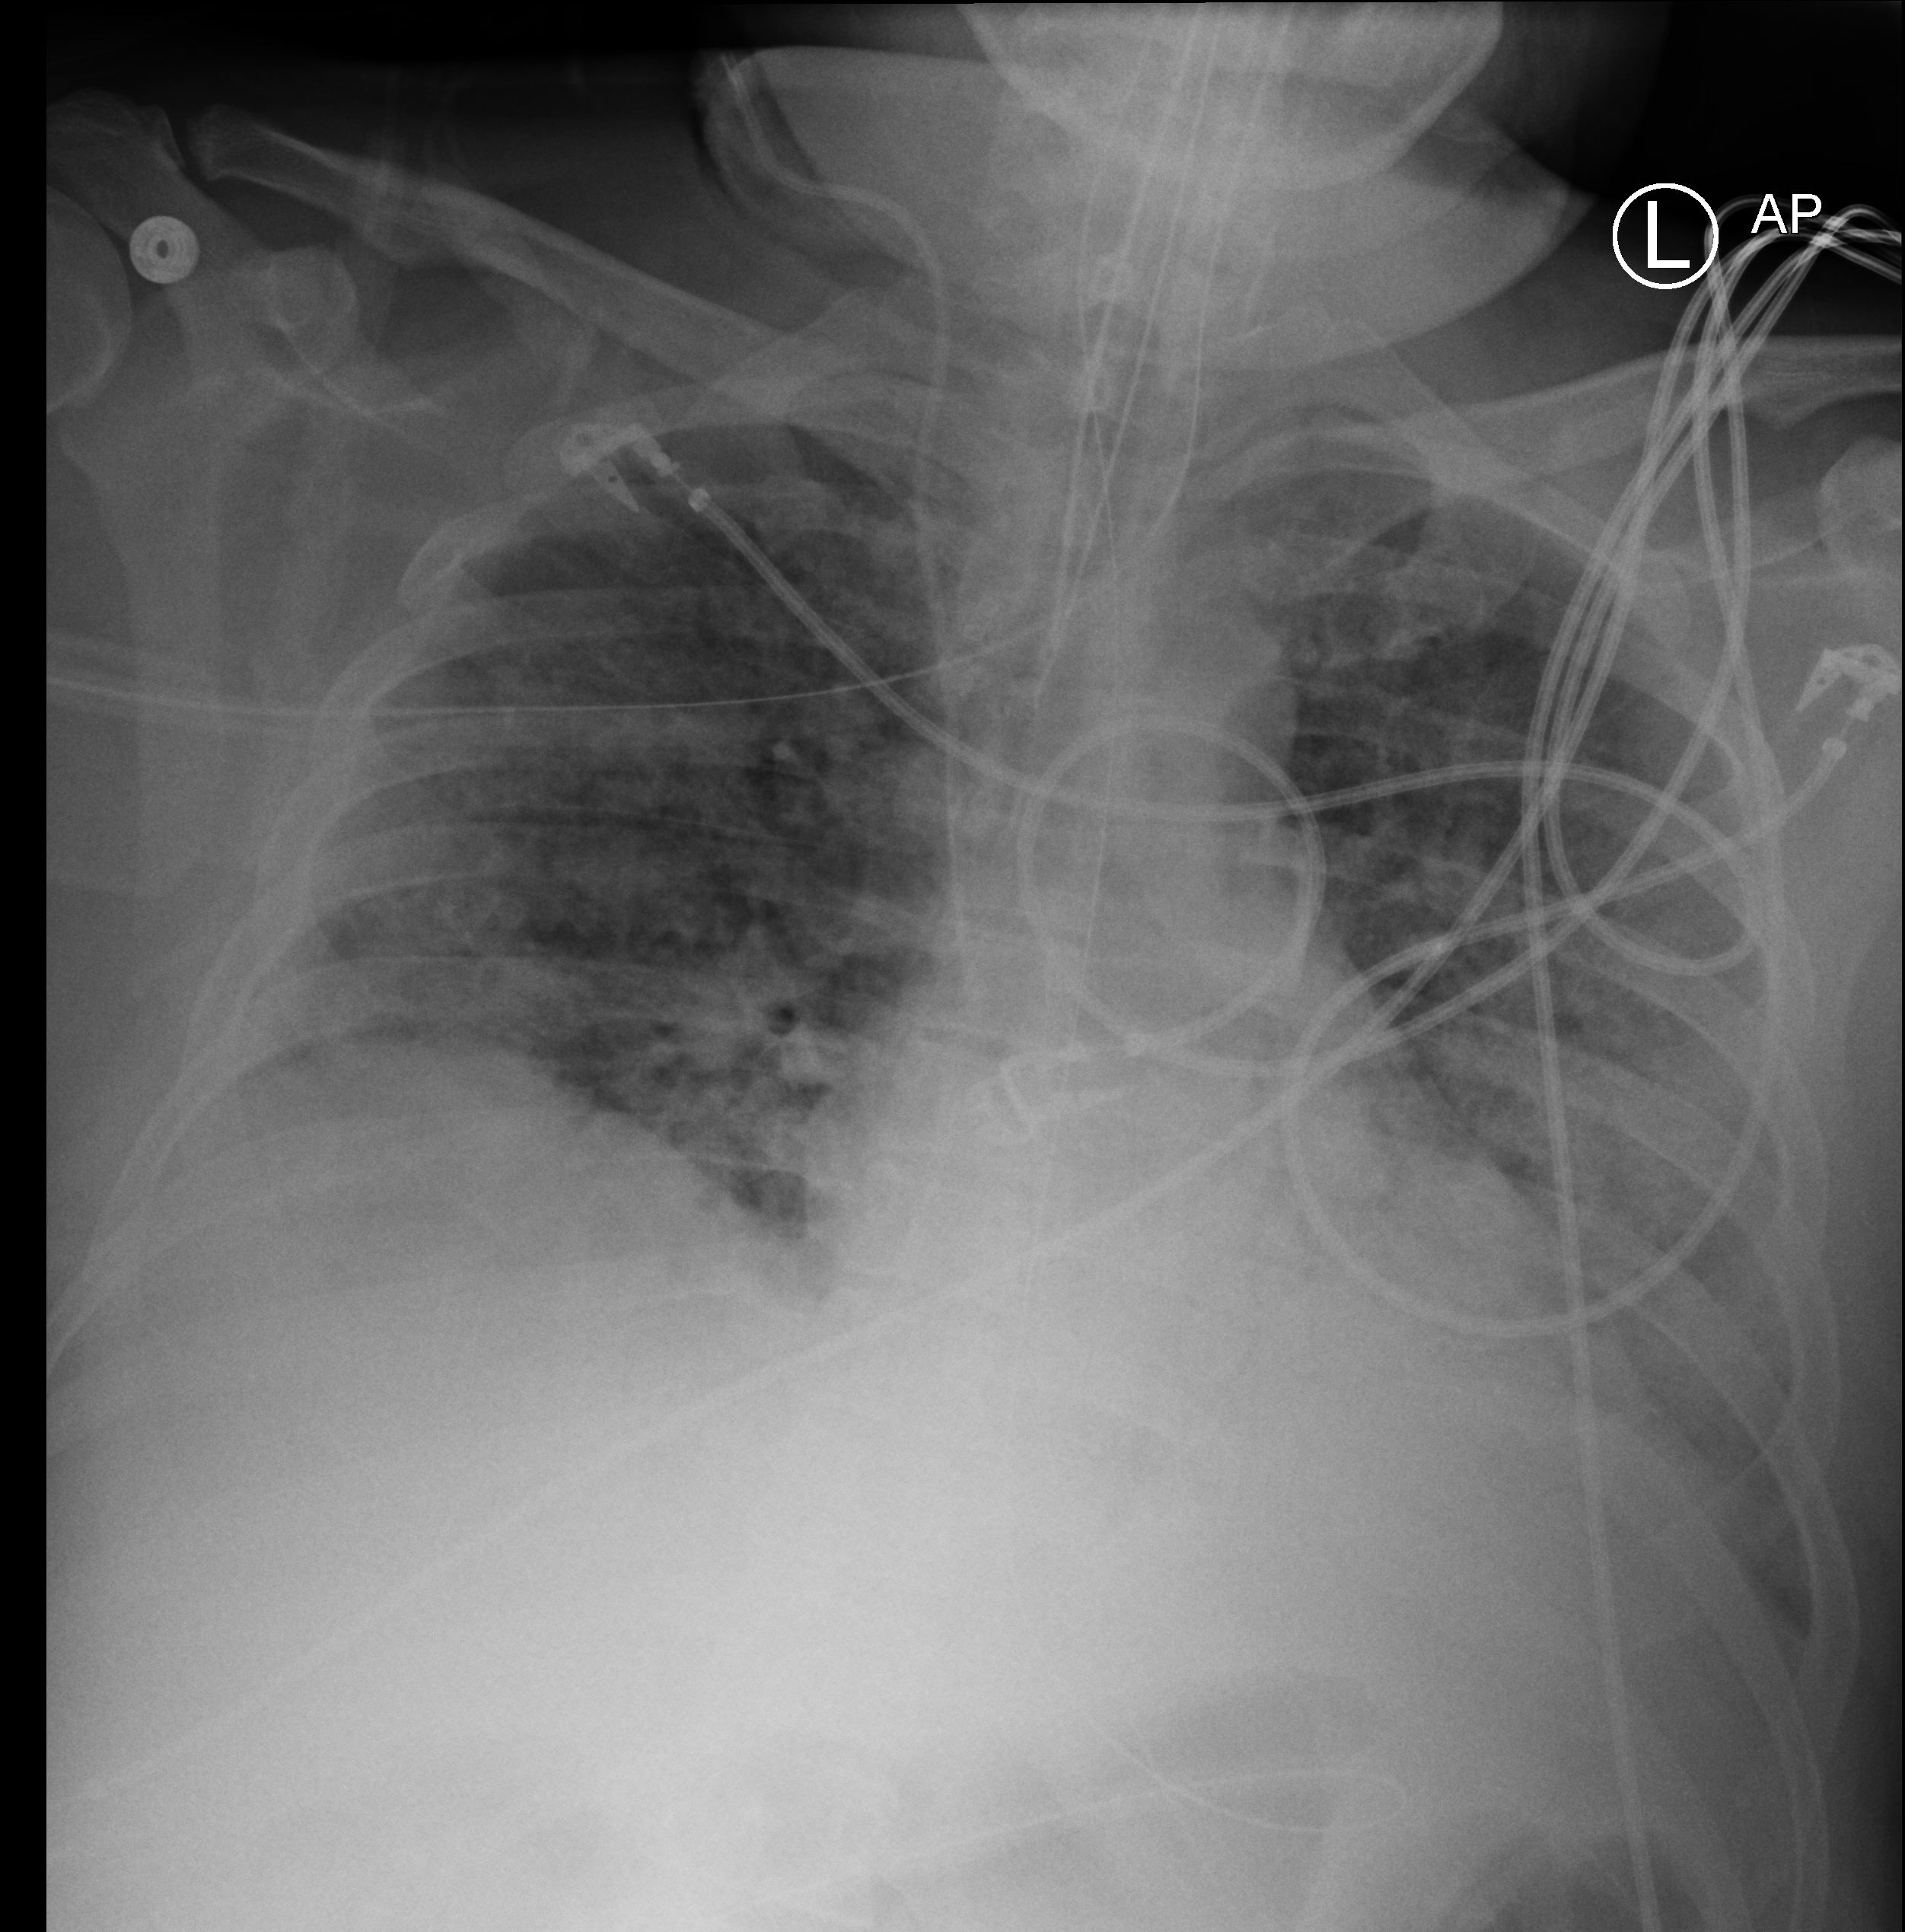
Chest X-ray (portable); anteroposterior (AP) projection. Patient hospitalised with COVID-19; male, aged 18–59 years.
Hospital-stay facts (about this admission, not read from this image; timing relative to this image not recorded):
- admitted to intensive care during this hospital stay: yes
- diabetes (admission record): no